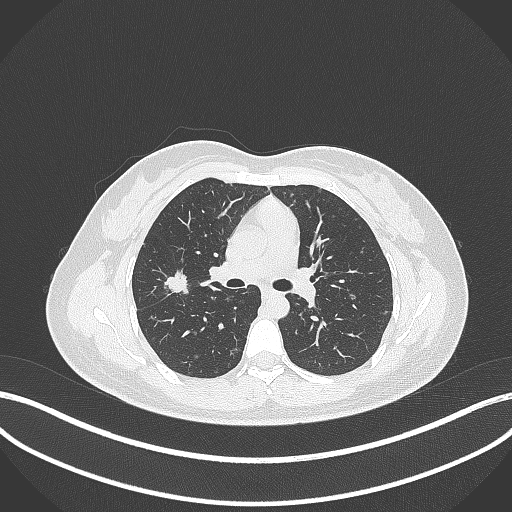
Chest CT, one axial slice. Position 201 of 307 along the scan axis. Reconstruction kernel B70f. 120 kVp. Lung window (W 1500 / L -600 HU). 1 mm slice thickness. 512 × 512 image matrix, field of view 400 × 400 mm. Patient: female, 33 years. Case-level facts recorded for this patient, not image findings: clinical TNM (as recorded): T1c N0 M0; histopathological grade: G2-G3.
Annotated regions visible in this slice (rectangle marked by the reading radiologist):
- lung tumour (recorded histology: adenocarcinoma): bounding box (x1, y1, x2, y2) in pixels: (162, 264, 189, 298)